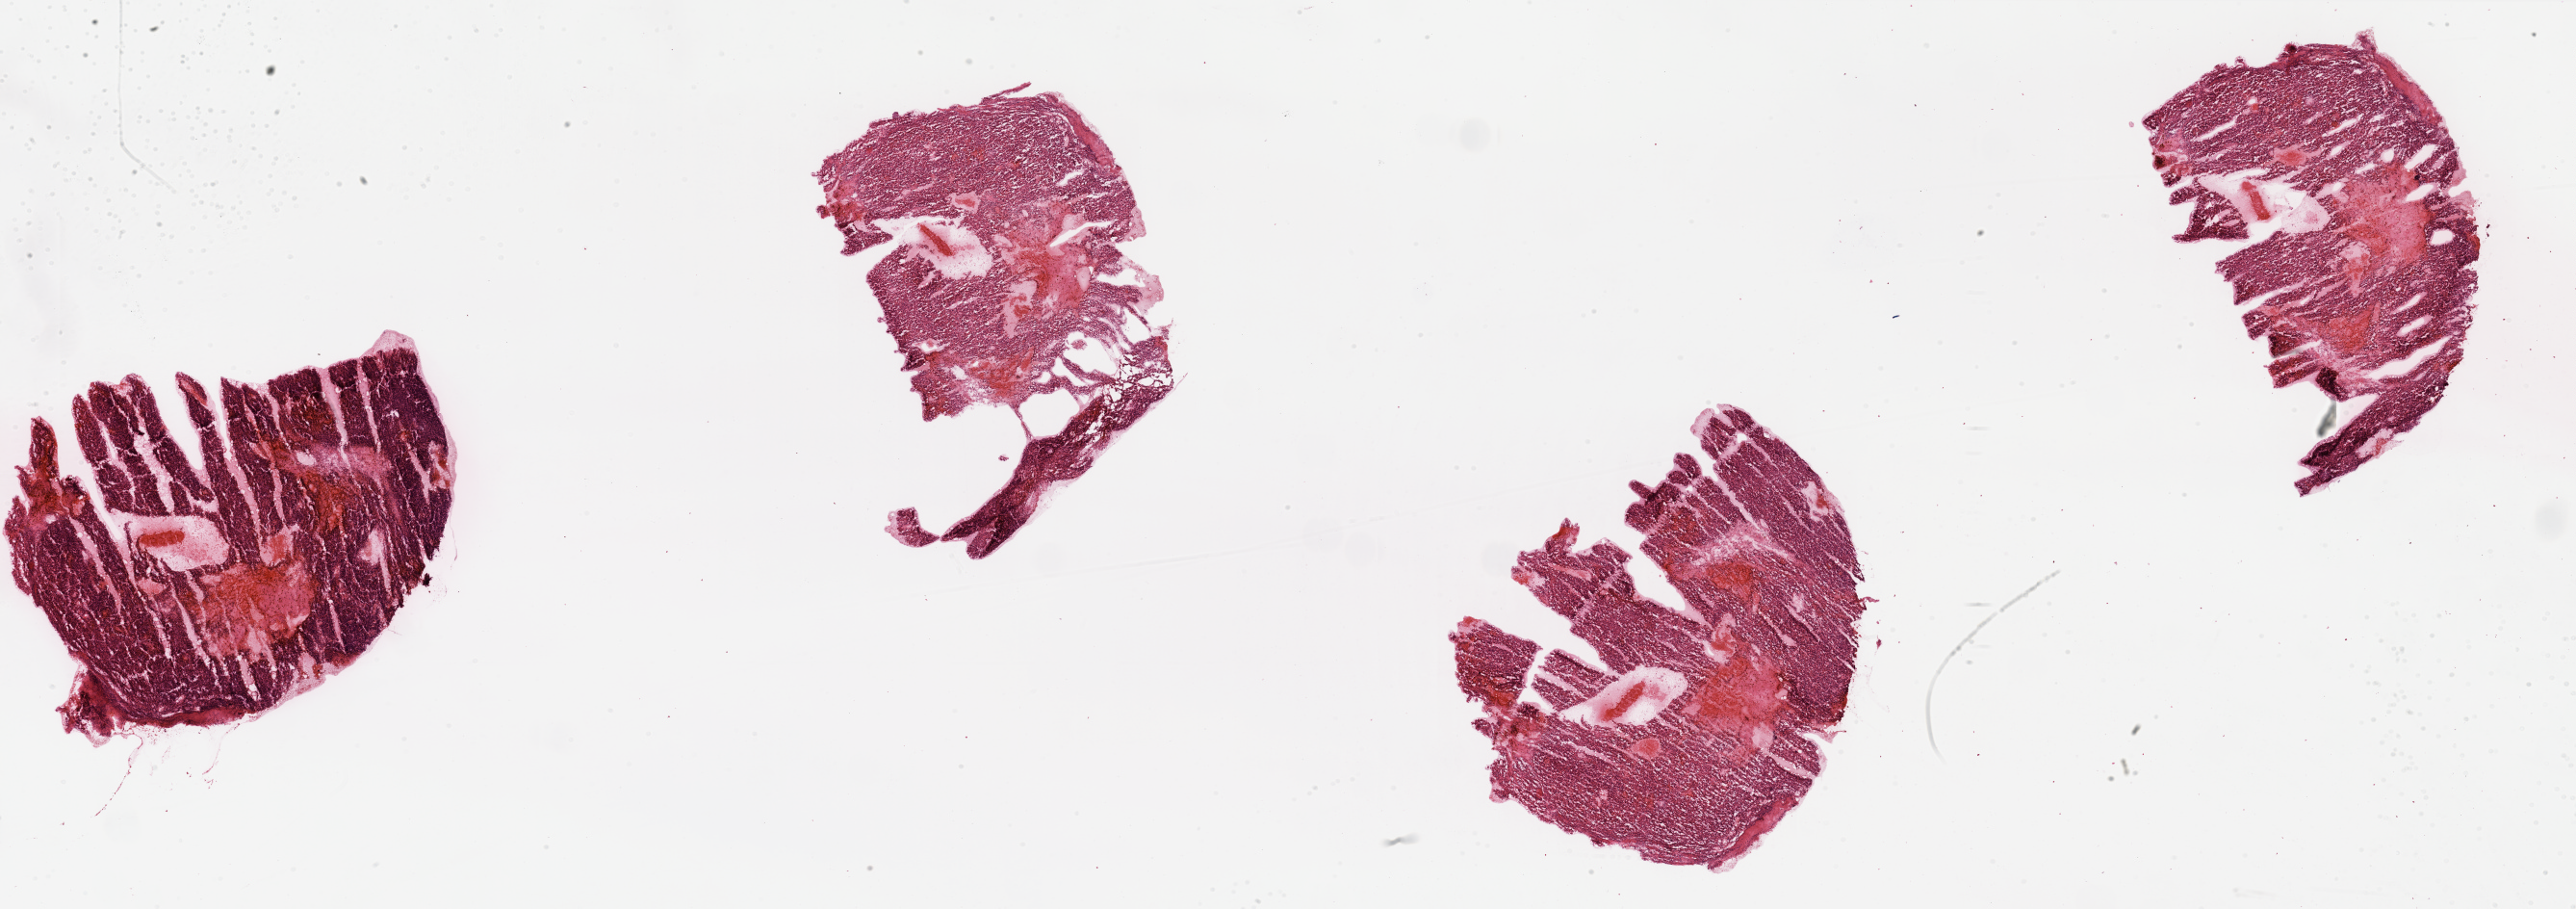
Whole-slide histology image, Hematoxylin and eosin (H&E) stained, shown as a low-resolution overview of the whole scanned area (about 42.3 x 14.9 mm, acquisition: 20x scan), tumour tissue sample, sampled site: kidney. Patient: male, age 66 years. Histologic grade: G2 (moderately differentiated). Slide review estimates, as recorded: tumour nuclei 85%, necrosis 15%.
• histologic diagnosis: Renal cell carcinoma, NOS
• AJCC pathologic stage: I
• primary tumour site (as recorded): upper pole